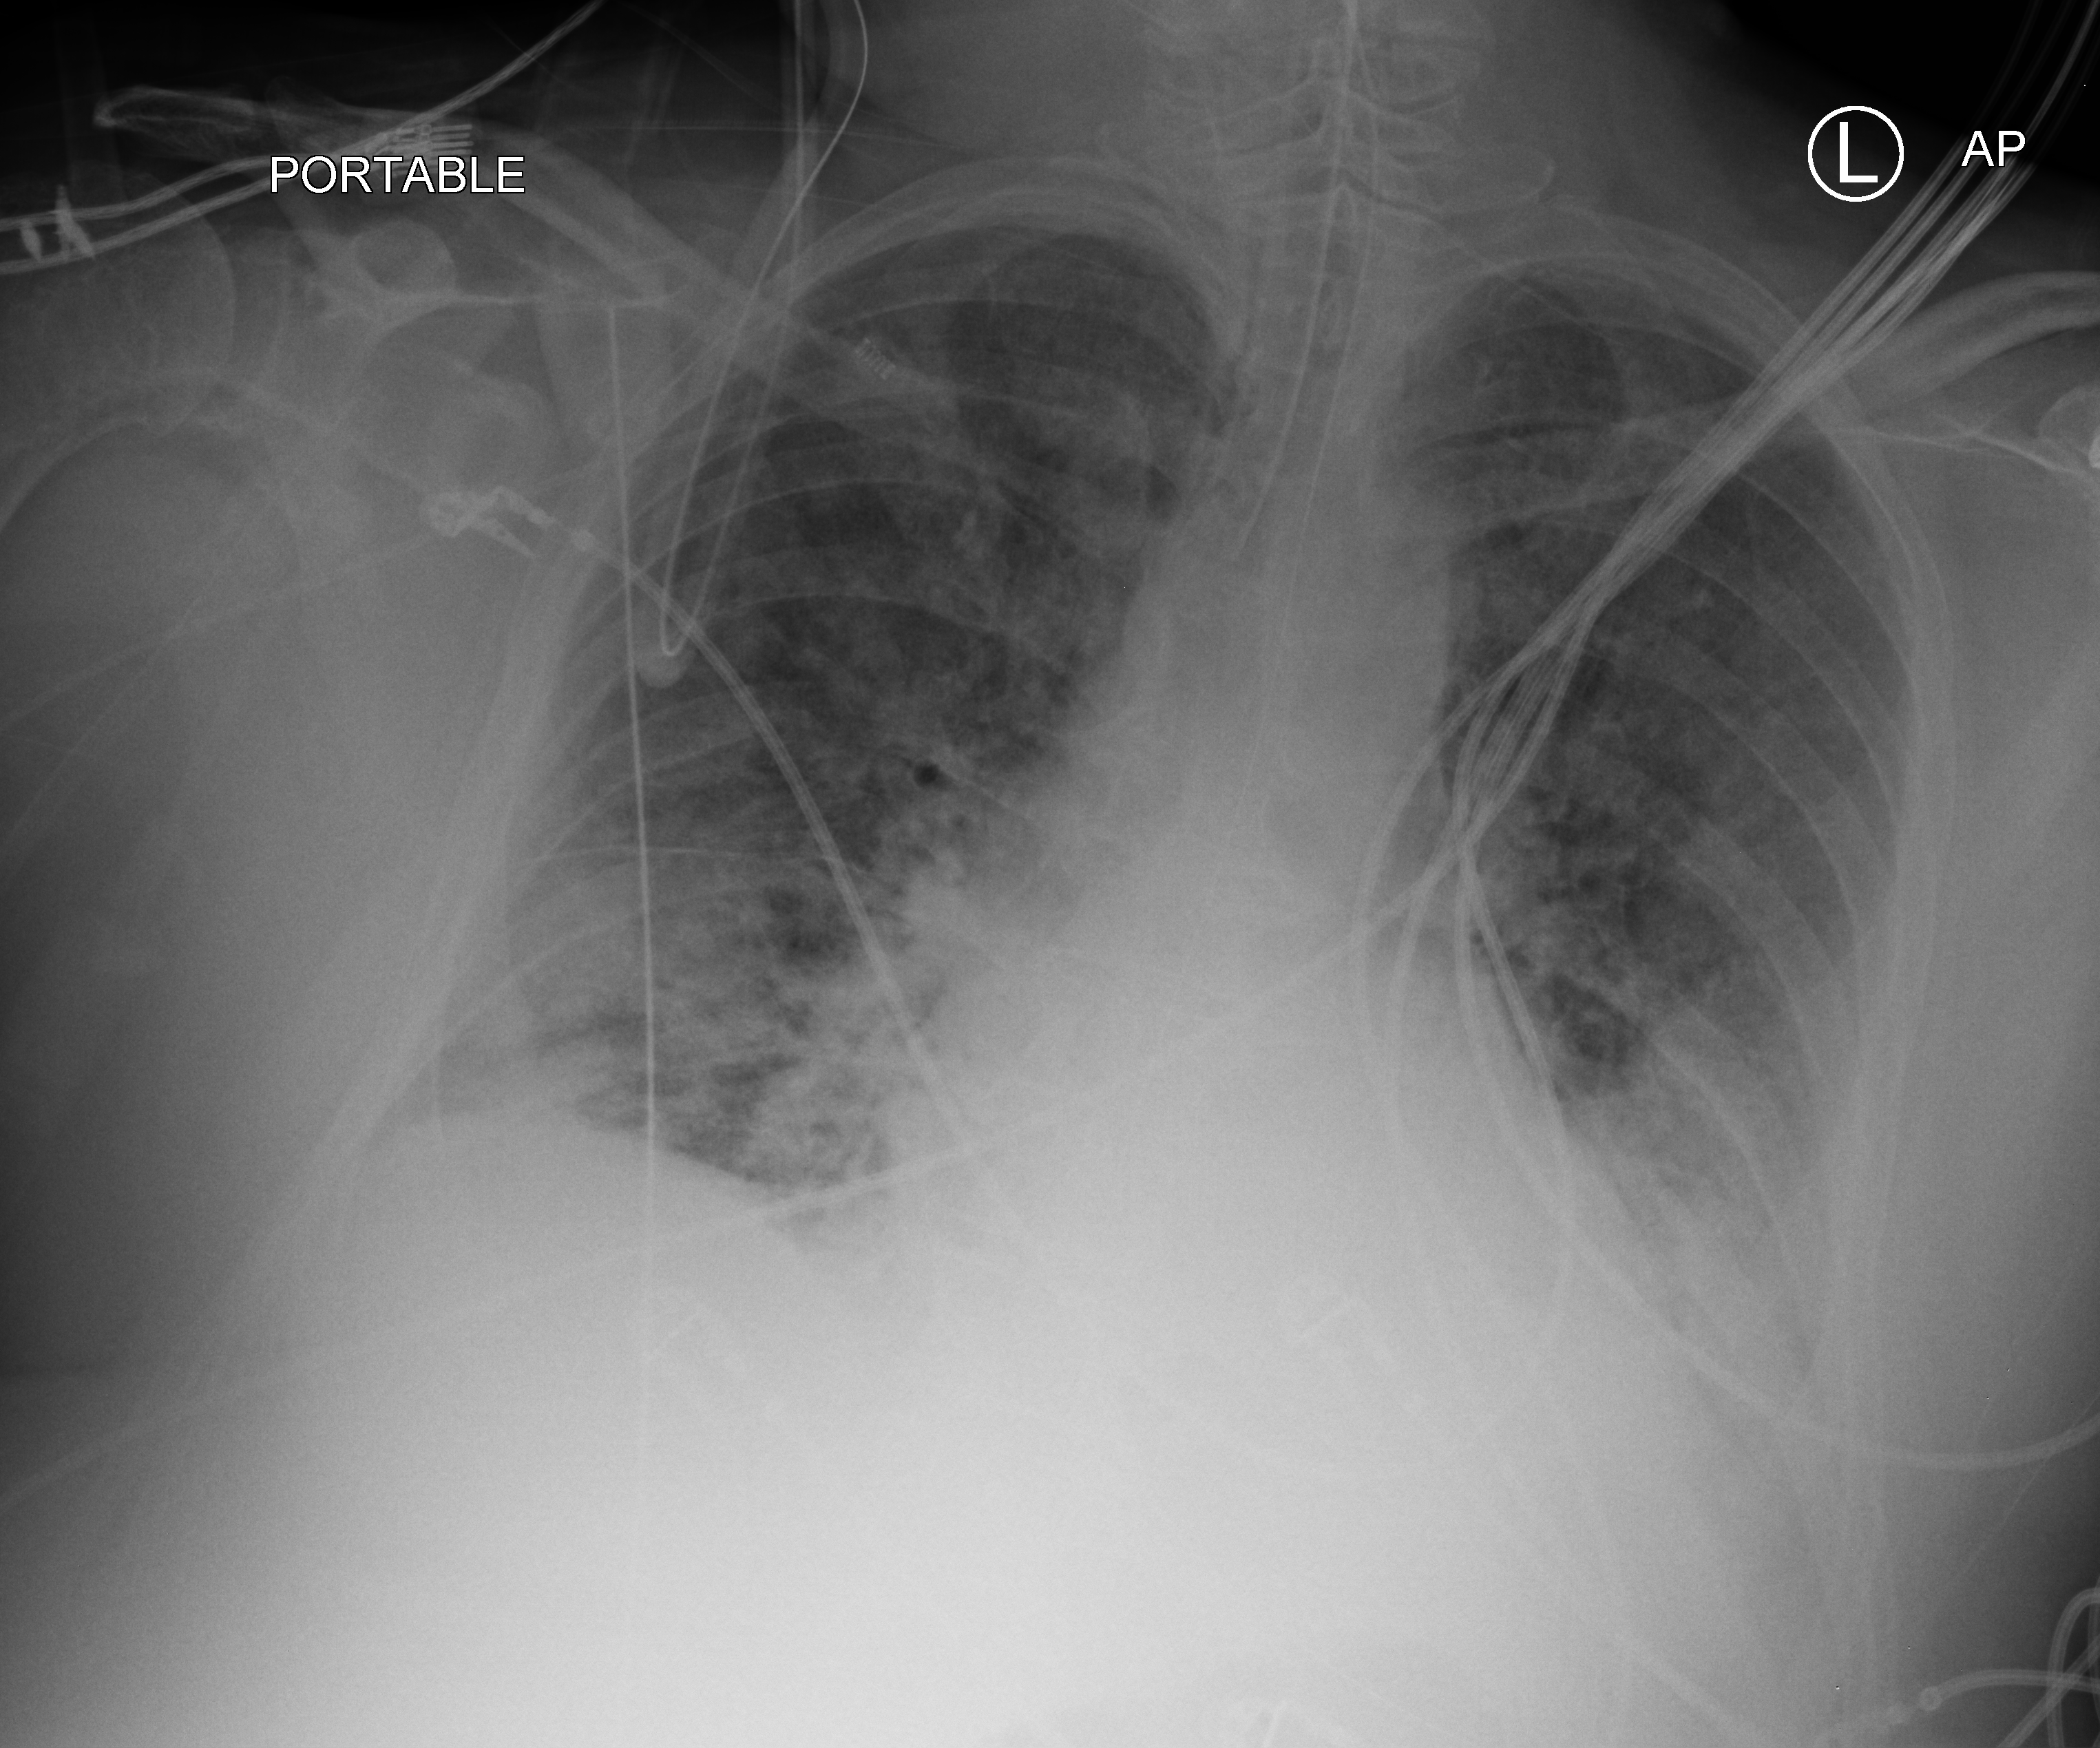
Chest X-ray (portable), anteroposterior (AP) projection. Male patient hospitalised with COVID-19, age 60–74 years.
Hospital-stay facts (about this admission, not read from this image; timing relative to this image not recorded): mechanically ventilated during this hospital stay: yes; admitted to intensive care during this hospital stay: yes.